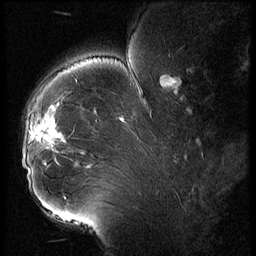
Breast MRI (dynamic contrast-enhanced), one sagittal slice. Slice 42 of 56 in the series (ordered by position). 3 images stored at this slice position (order not interpretable as contrast timing). 1.5 T. TE 4.2 ms, TR 9 ms. 256 × 256 image matrix. Female patient, age 43 years. From the clinical record (not read from this slice): setting: breast cancer imaged before/during neoadjuvant chemotherapy; receptor status: HER2-positive.
Outlined on this slice (semi-automatic segmentation, software-assisted and operator-edited):
- analysis volume of interest (the breast-tissue region the enhancement analysis was run in; not a lesion): bounding box [x1, y1, x2, y2] px = [23, 92, 74, 211]
- tumour enhancement mask (voxels above the 140 % enhancement threshold inside the analysis volume of interest): [32, 125, 63, 142]